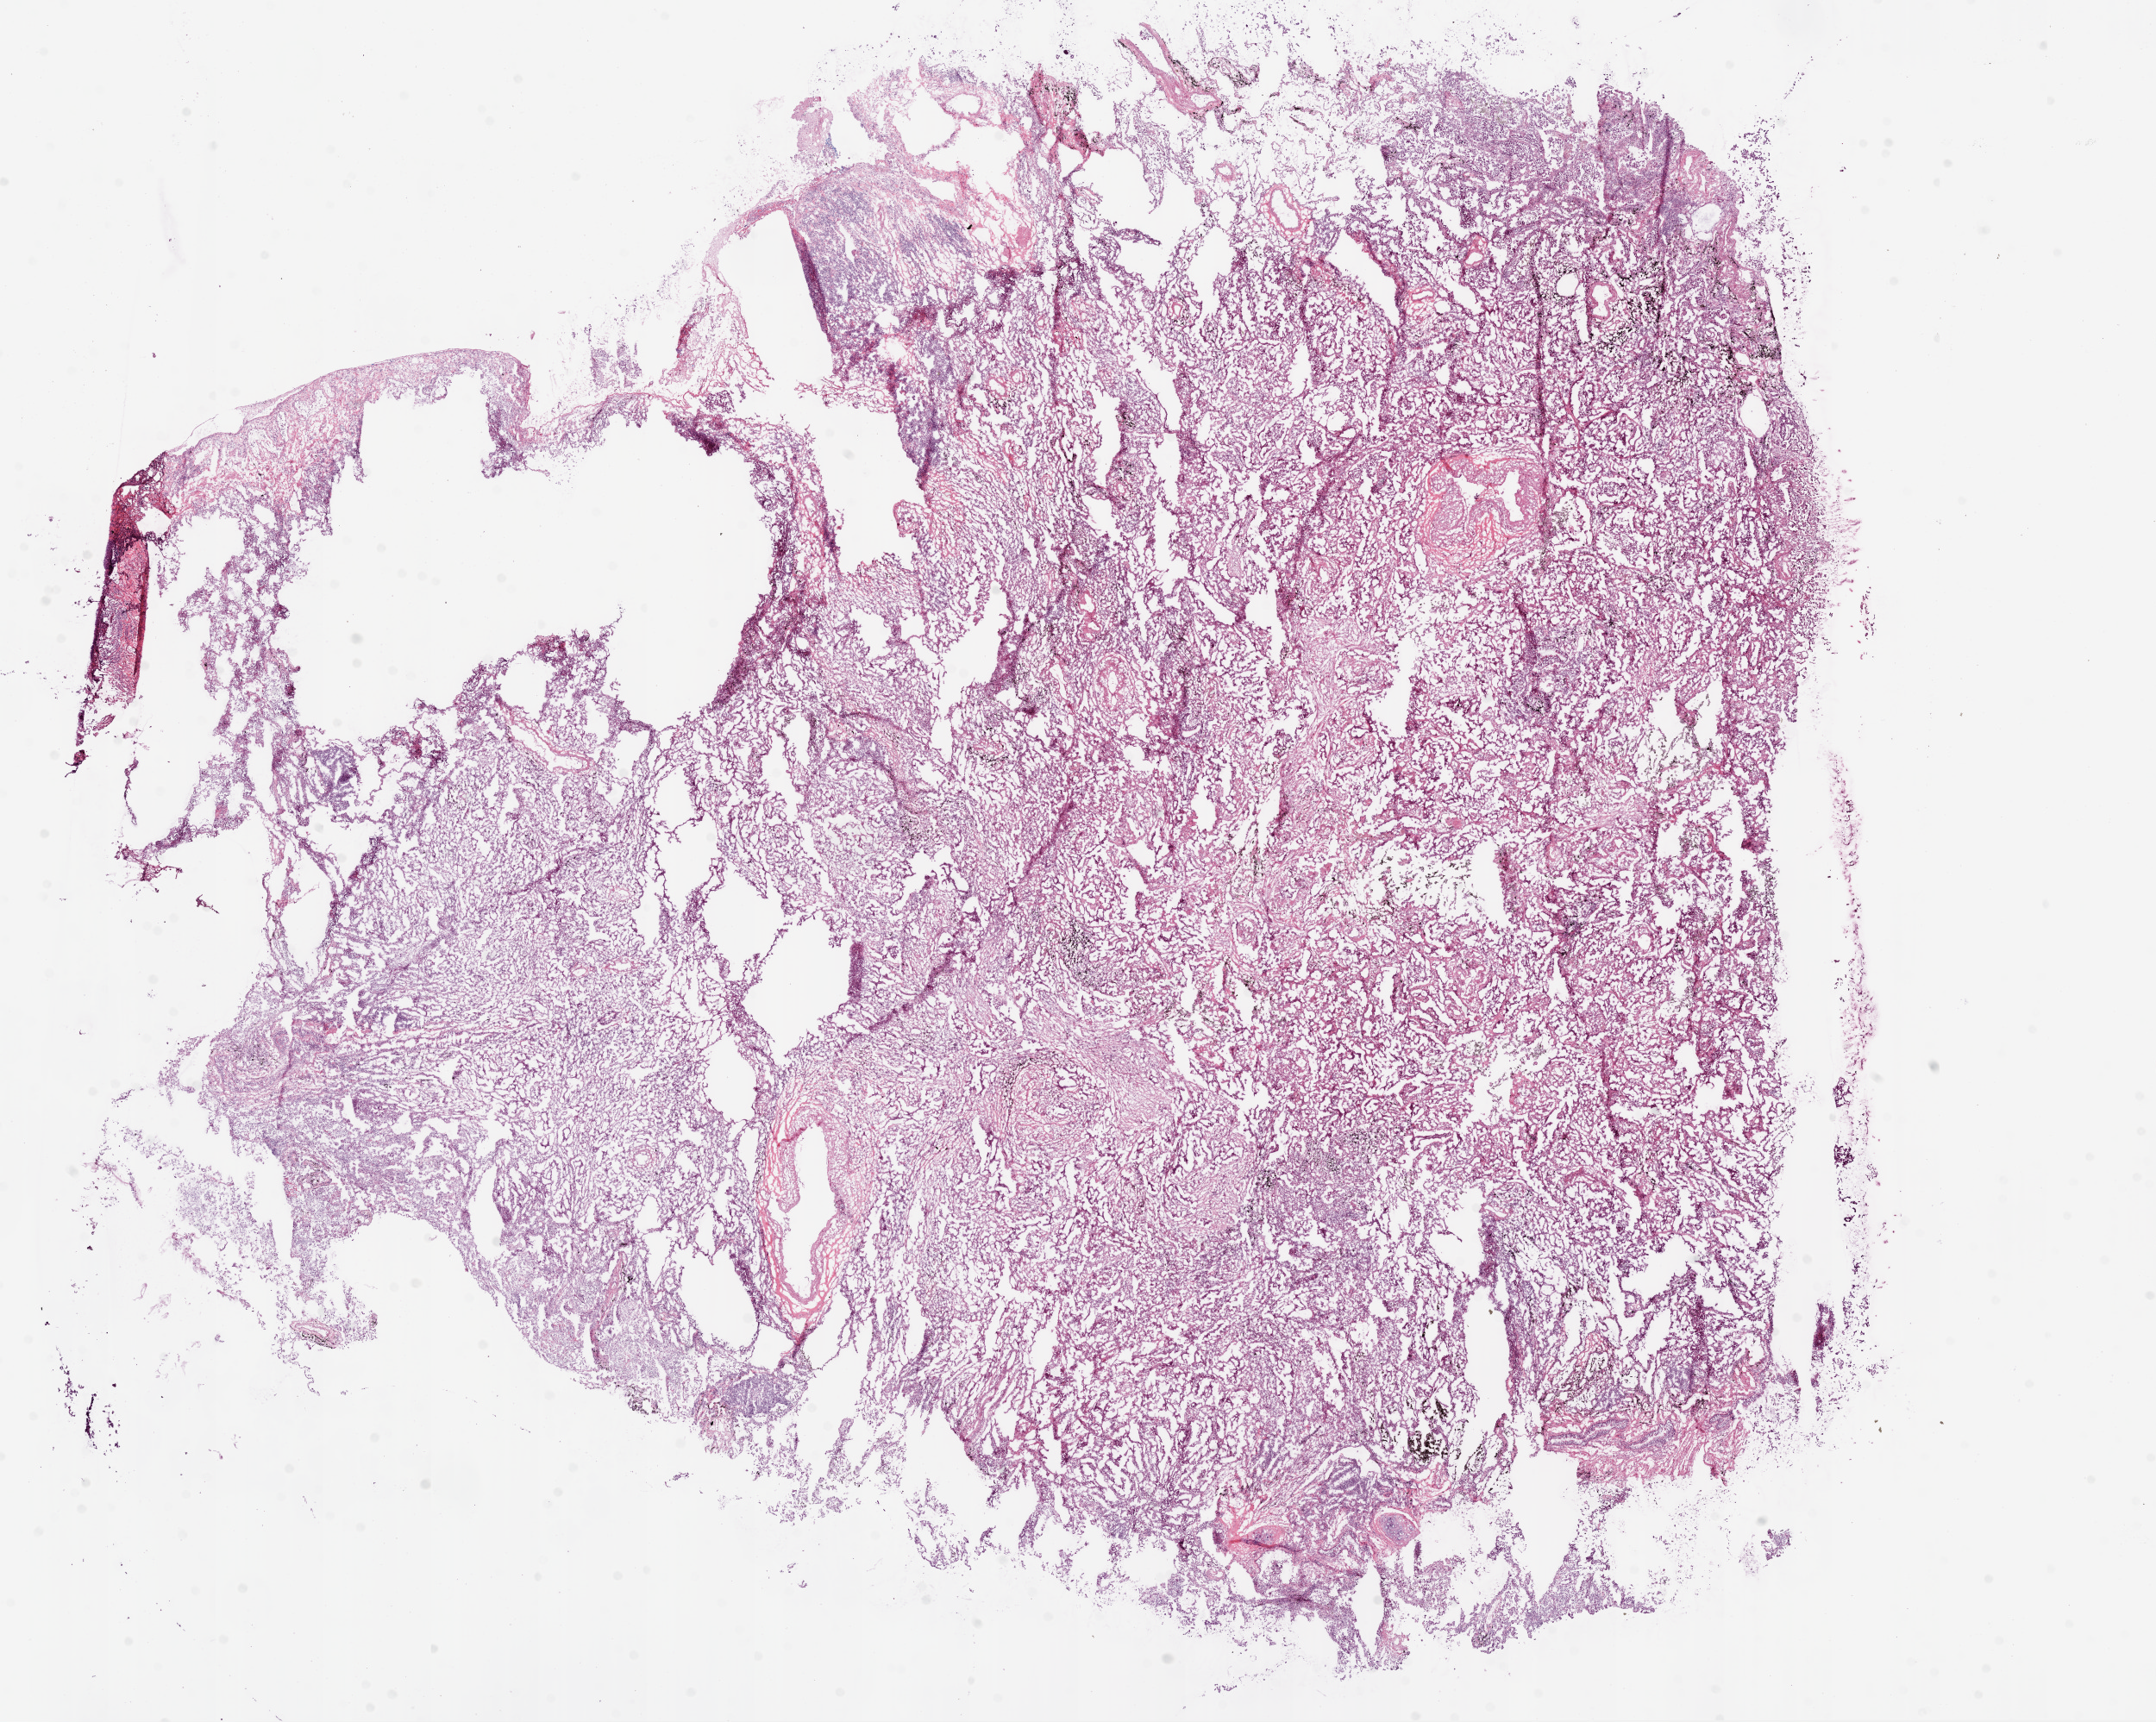
Digitized H&E-stained tissue section (whole slide), a low-resolution overview of the entire scanned area, about 20.1 x 16.0 mm (from a 20x scan), frozen section from the bottom of the tissue portion, lung, primary tumour sample. Female patient; age at initial diagnosis 57 years.
Histologic diagnosis: Adenocarcinoma, NOS (lower lobe, lung).